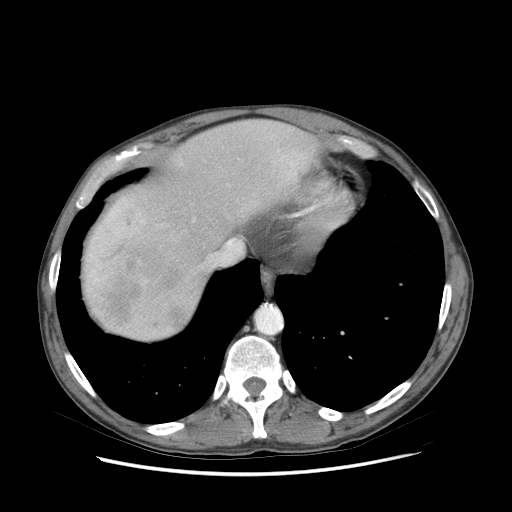
Contrast-enhanced abdominal CT (liver protocol), one axial slice; soft-tissue window (W 400 / L 40 HU); 512 × 512 image matrix. Case-level facts recorded for this patient, not image findings: diagnosis: hepatocellular carcinoma (patient treated with transarterial chemoembolisation; whether this scan precedes or follows treatment is not stated here); TNM stage (as recorded): Stage-IIIB; Child-Pugh class: A; tumour nodularity: multinodular.
Annotated regions visible in this slice (semi-automatic segmentation, software-assisted and operator-edited):
- abdominal aorta: box from (x=257, y=306) to (x=281, y=333) px
- liver parenchyma outside the tumour (the mass and vessels are separate outlines, so this box may not span the whole liver): (x=82, y=120)–(x=318, y=340)
- mass: (x=95, y=244)–(x=188, y=323)
- liver vessels: (x=89, y=157)–(x=296, y=285)